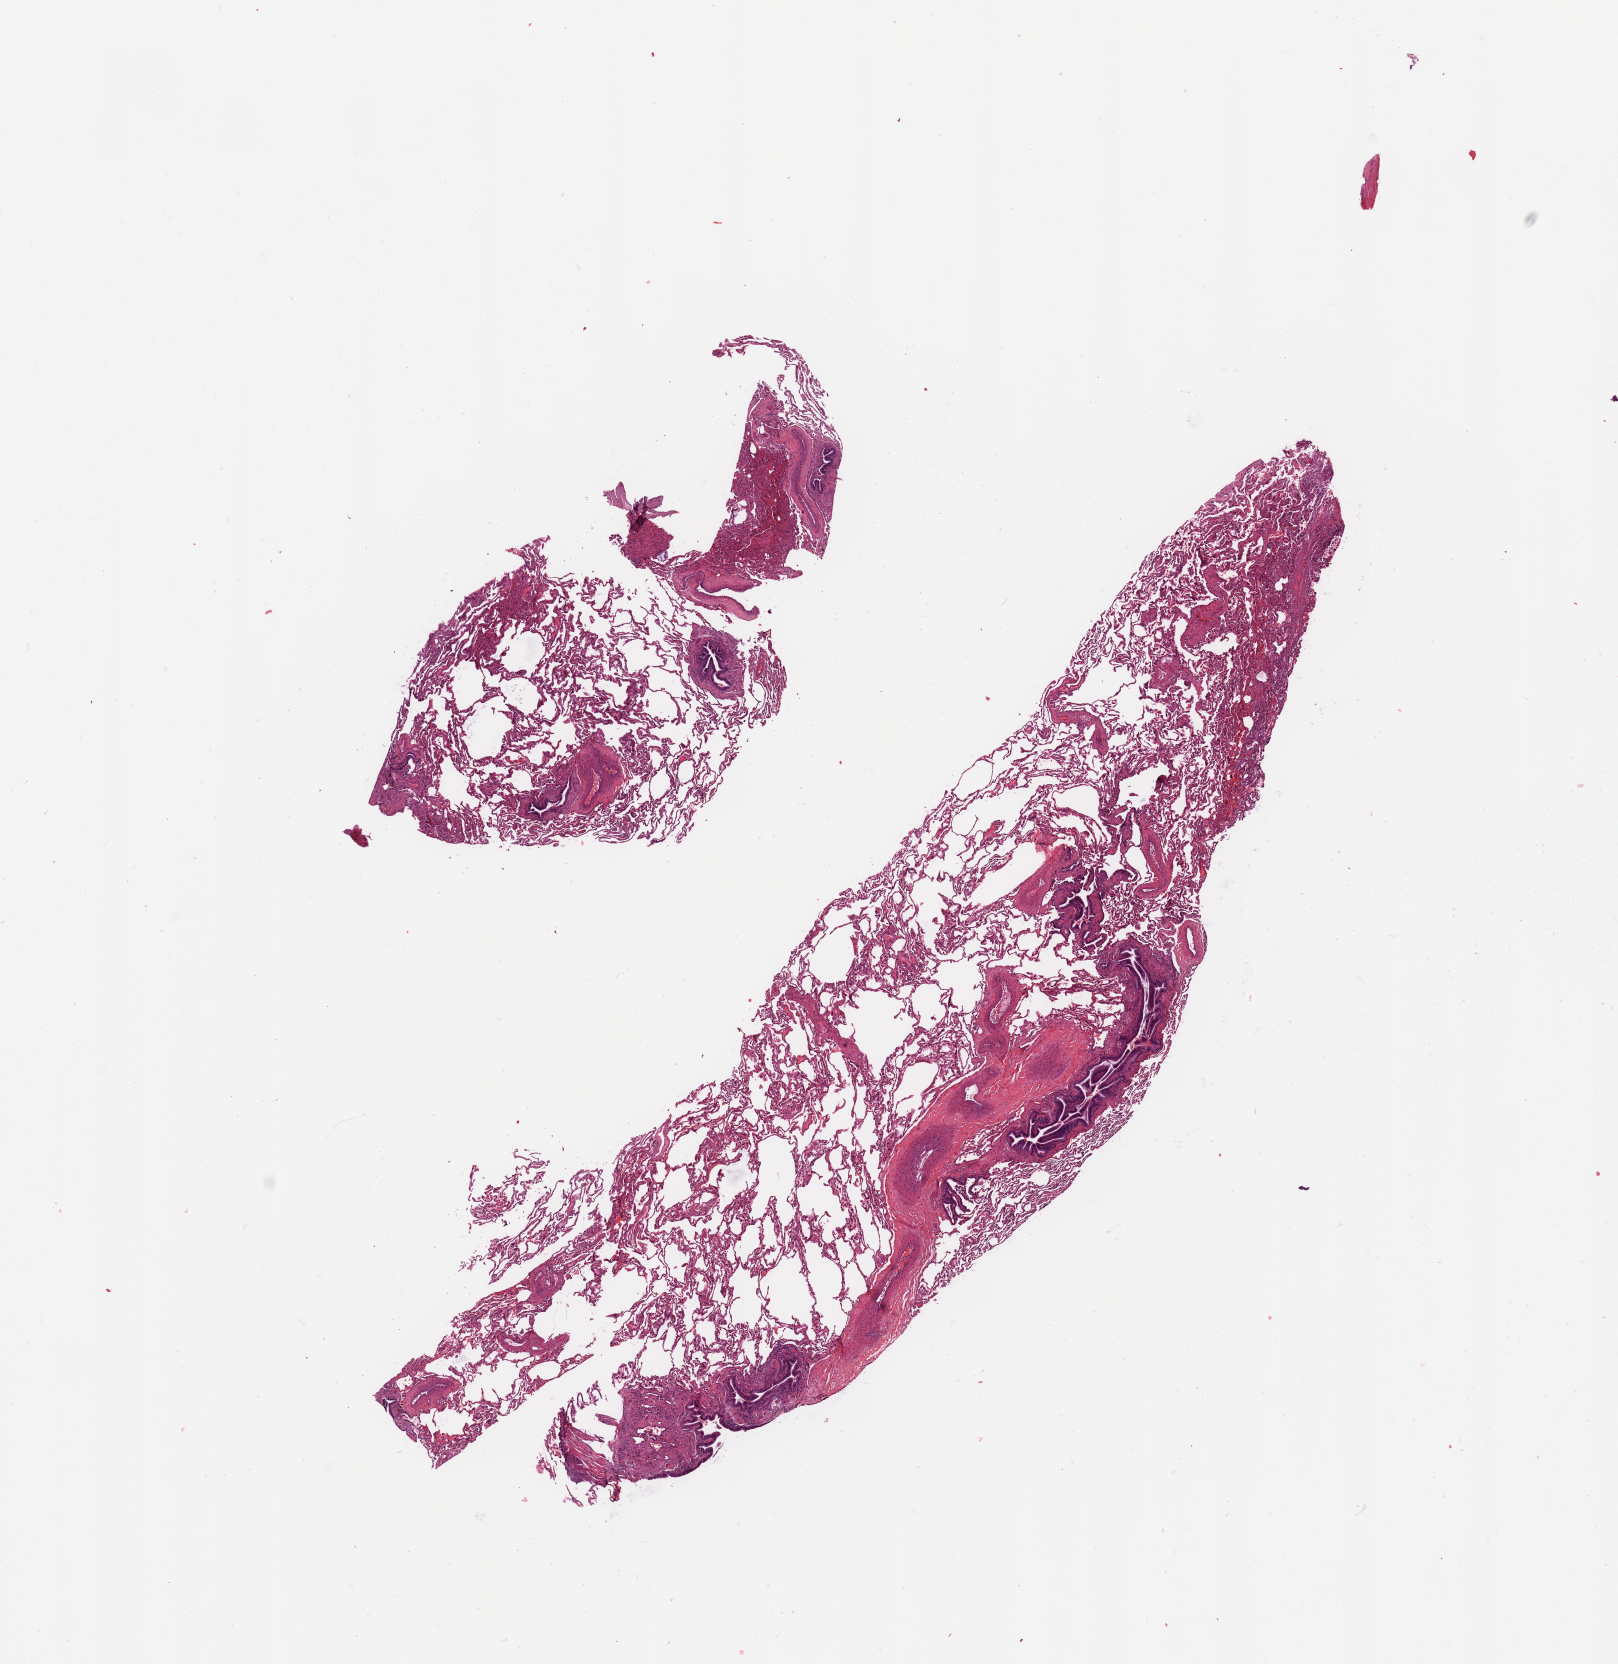
Digitized H&E-stained tissue section (whole slide), whole scanned area (about 12.8 x 13.2 mm, acquisition: 20x scan) shown as a low-resolution overview, lung, normal (non-tumour) tissue. Male, 67 y/o.
This section: normal (non-tumour) tissue from the same patient. Patient diagnosis: Squamous cell carcinoma, NOS.